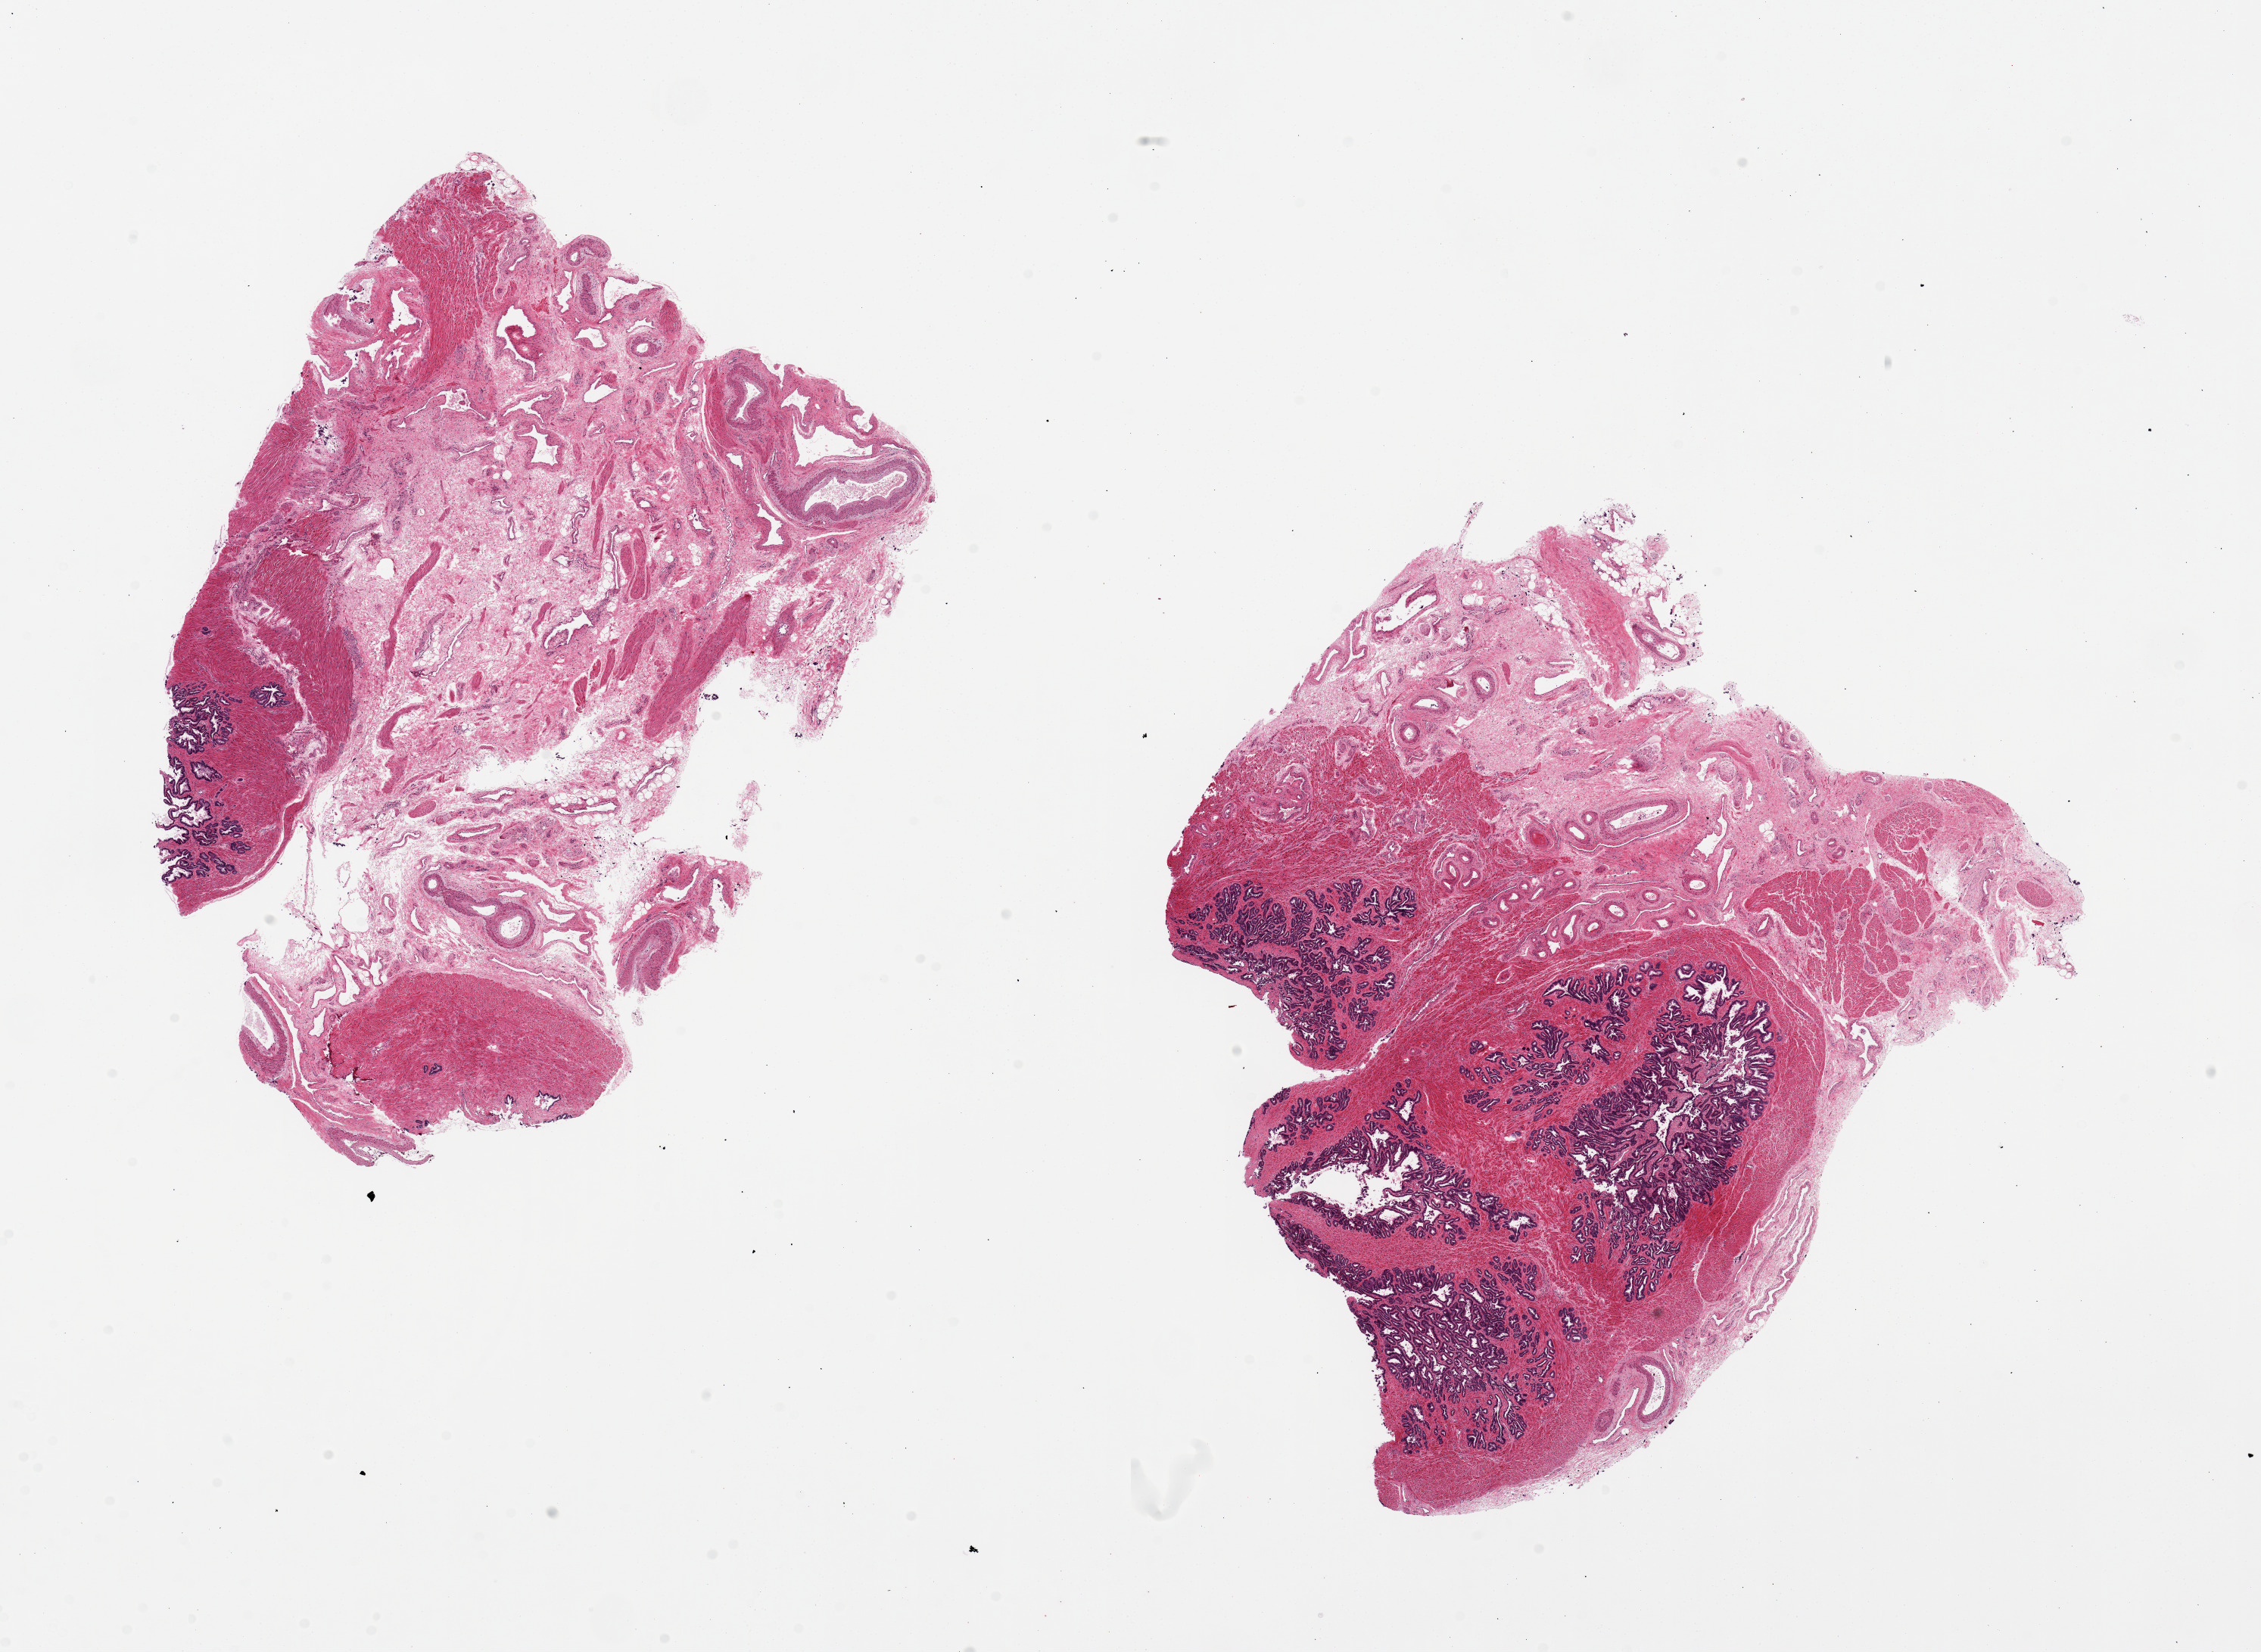
Digitized haematoxylin and eosin-stained section, brightfield — a low-resolution overview of the entire scanned area, about 23.6 x 17.3 mm; PAXgene-fixed, paraffin-embedded tissue; sampled site (target tissue): prostate; donor tissue sample. Male donor.
Reviewer comment on this tissue sample: 2 pieces, 10x7.5 and 9x7mm; not prostate but seminal vesicle/stroma.